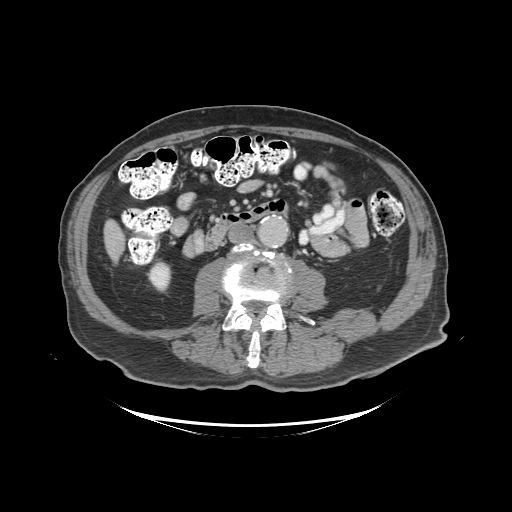
Contrast-enhanced abdominal CT (liver protocol), one axial slice. Slice 23 of 99 in the series (ordered by position). Soft-tissue window (W 400 / L 40 HU). 2.5 mm slice thickness. 512 × 512 image matrix. From the clinical record (not read from this slice): diagnosis: hepatocellular carcinoma (patient treated with transarterial chemoembolisation; whether this scan precedes or follows treatment is not stated here); TNM stage (as recorded): Stage-I; Child-Pugh class: A; tumour differentiation: moderately differentiated.
Structures marked on this image (semi-automatic segmentation, software-assisted and operator-edited):
- liver parenchyma outside the tumour (the mass and vessels are separate outlines, so this box may not span the whole liver): bounding box [x1, y1, x2, y2] px = [104, 220, 124, 260]